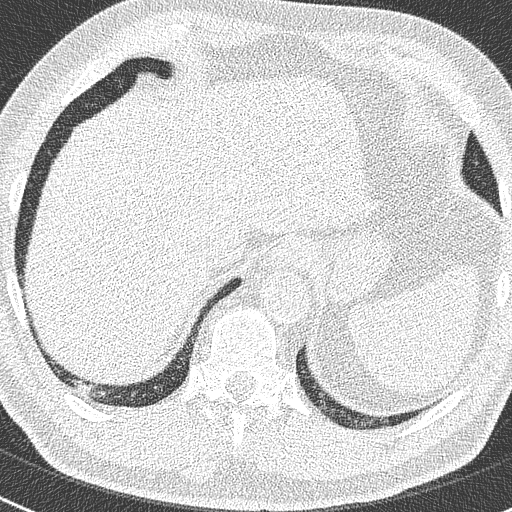
Axial slice from a low-dose chest CT screening exam. Second screening round (one year after baseline). Lung window (W 1500 / L -600 HU). Male, age 63 years at enrolment. Former smoker at enrolment.
• Lesion marked by an expert reader, bounding box [x1, y1, x2, y2] px = [67, 378, 100, 404].
• No non-calcified nodule or mass ≥4 mm was recorded by the screening reader at this exam.
• Official screen result: negative screen, no significant abnormalities.
• Lung cancer was diagnosed 262 days after this screen: adenocarcinoma, NOS, right lower lobe, moderately differentiated (G2), stage IIIB (AJCC 6th edition), 17 mm at pathology.